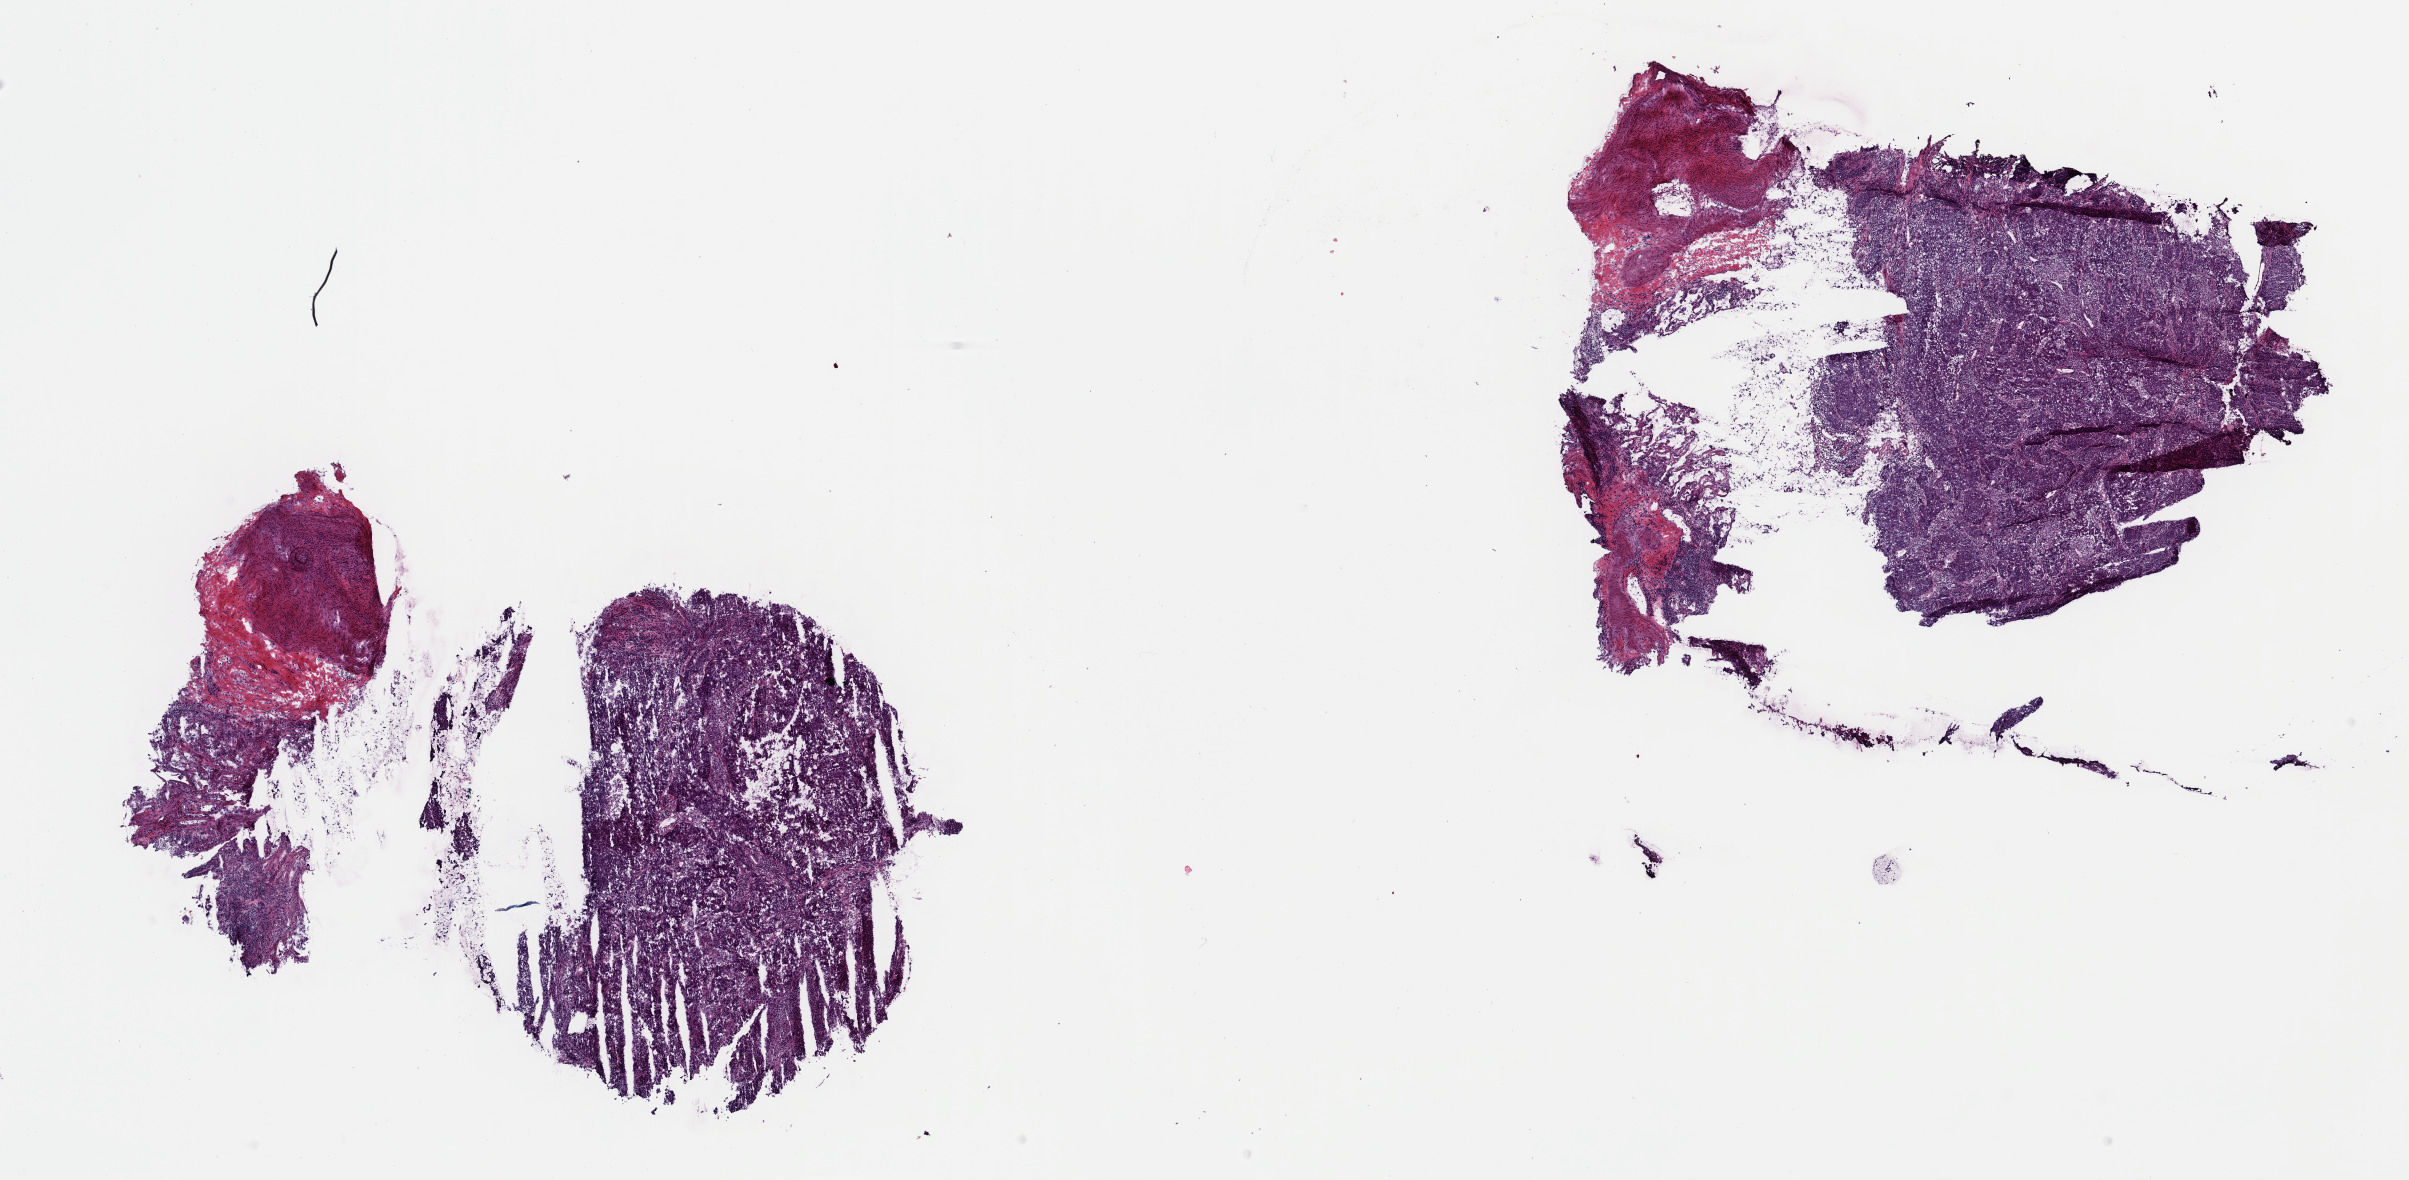
Digitized H&E-stained tissue section (whole slide) — a low-resolution overview of the entire scanned area, about 19.0 x 9.3 mm (slide scanned at 40x); frozen section from the top of the tissue portion; primary tumour sample from the lung. Patient: female, age at initial diagnosis 67 years. Composition of this section per pathologist review: tumour cells 85%, tumour nuclei 60%.
Histologic diagnosis: Squamous cell carcinoma, NOS (upper lobe, lung).